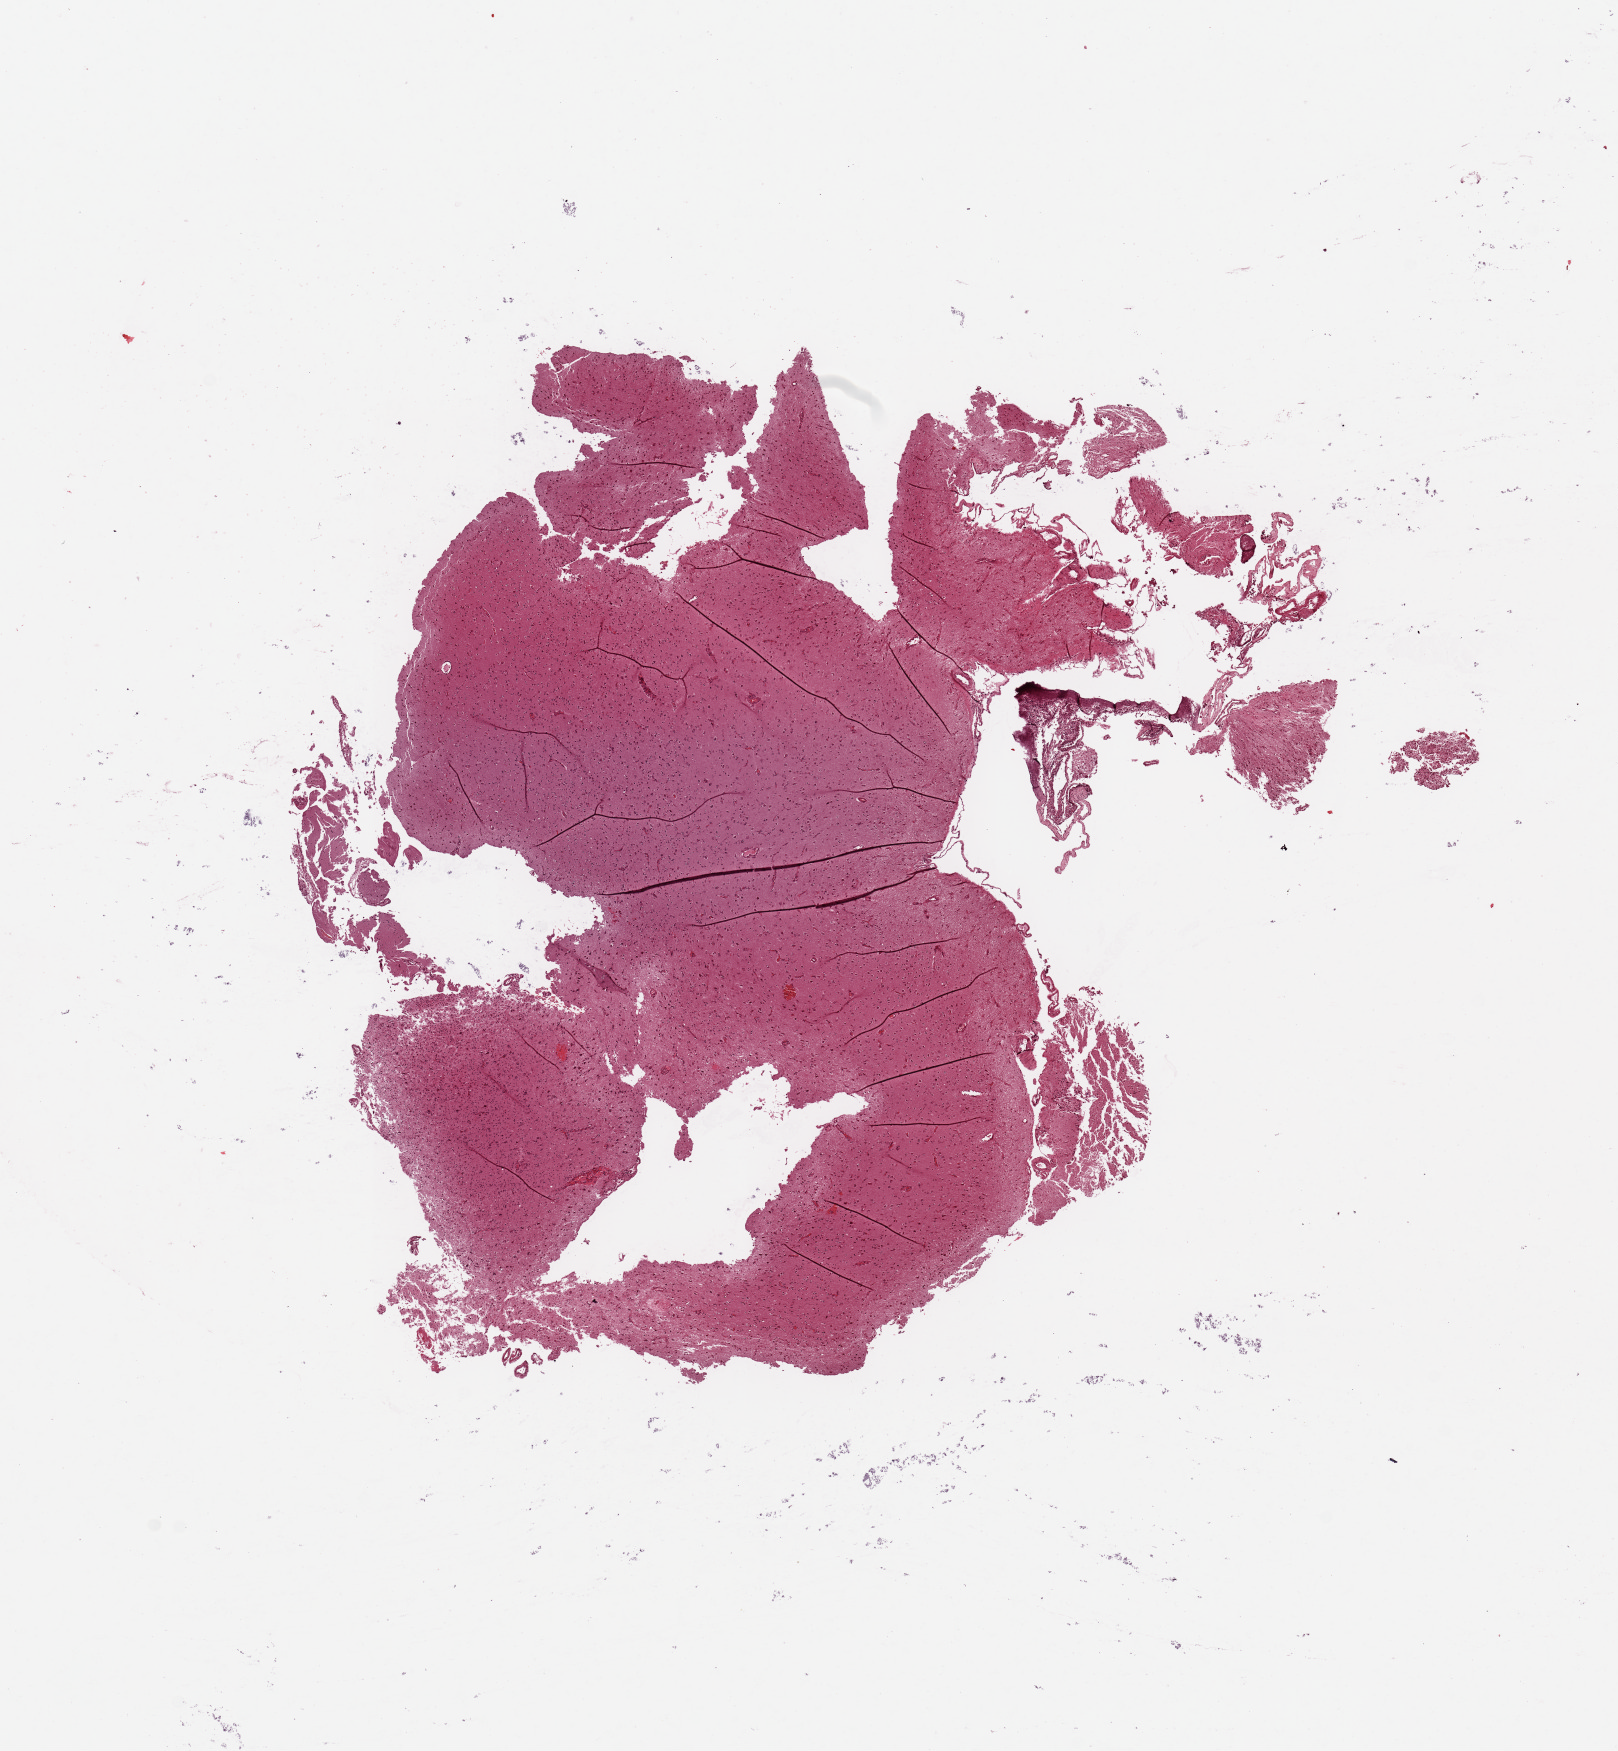
Whole-slide histology image, H&E, shown as a low-resolution overview of the whole scanned area (about 12.8 x 13.8 mm, slide scanned at 20x), brain, tumour tissue. Patient: male, age 60 years.
Diagnosis: Glioblastoma. Primary tumour site (as recorded): temporal lobe.